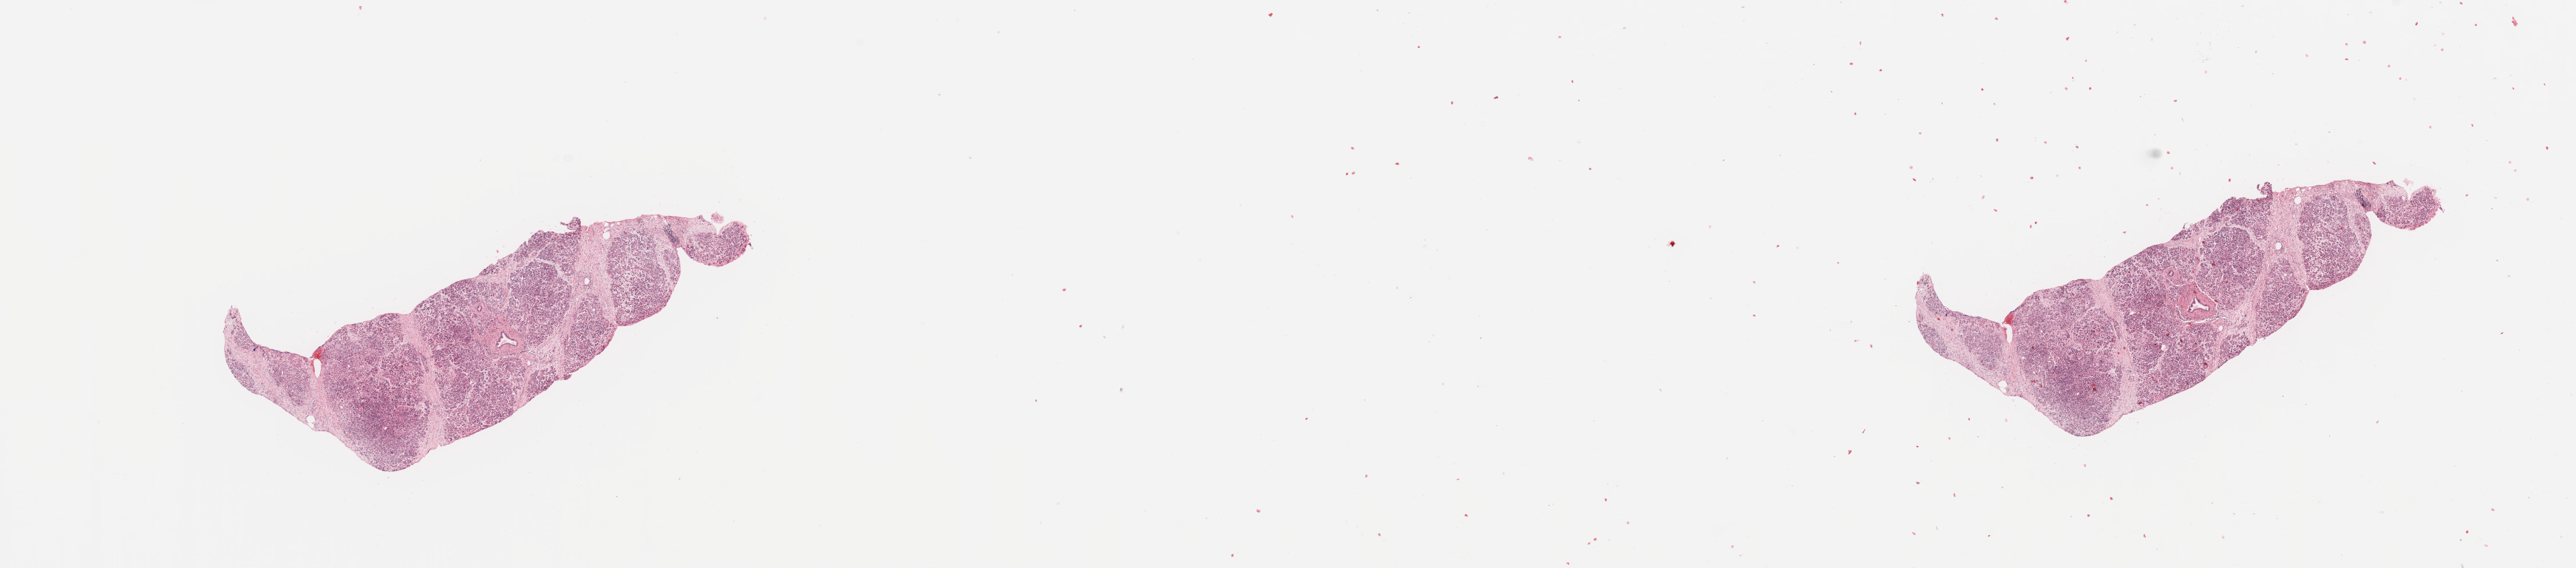
H&E-stained whole-slide image — whole scanned area (about 27.6 x 6.1 mm, slide scanned at 20x) shown as a low-resolution overview; pancreas, normal (non-tumour) tissue. Female, 62 y/o.
• this section: normal (non-tumour) tissue from the same patient
• patient diagnosis: Infiltrating duct carcinoma, NOS